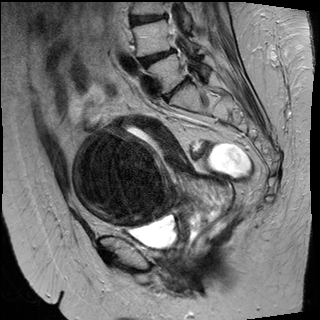
Pelvic MRI for cervical cancer, one sagittal slice. Position 23 of 50 along the scan axis. T2-weighted. 1.5 T. TE 89 ms, TR 4880 ms. 320 × 320 image matrix, field of view 260 × 260 mm. Patient: female, 50 years.
Outlined on this slice (expert manual segmentation):
- uterus and cervix: box from (x=75, y=117) to (x=233, y=240) px